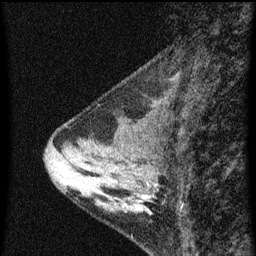
Breast MRI (dynamic contrast-enhanced), one sagittal slice. Position 23 of 60 along the scan axis. Dynamic contrast-enhanced series, image 2 of 3 at this slice position (ordered by acquisition). 1.5 T. TE 4.2 ms, TR 8 ms. 2 mm slice thickness. 256 × 256 image matrix, field of view 180 × 180 mm. Patient: female, 34 years.
Outlined on this slice (semi-automatically segmented with operator editing):
- analysis volume of interest (the breast-tissue region the enhancement analysis was run in; not a lesion): bounding box (x1, y1, x2, y2) in pixels: (70, 138, 163, 215)
- tumour enhancement mask (voxels above the 70 % enhancement threshold inside the analysis volume of interest): (140, 196, 149, 203)